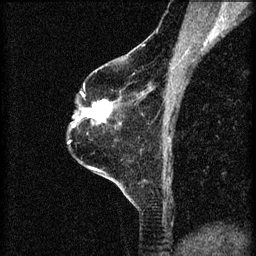
Breast MRI (dynamic contrast-enhanced), one sagittal slice; position 44 of 60 along the scan axis; 3 images stored at this slice position (order not interpretable as contrast timing); 1.5 T; TE 4.2 ms, TR 8.2 ms; 2 mm slice thickness; 256 × 256 image matrix, field of view 180 × 180 mm. Patient: female, 60 years.
Annotated regions visible in this slice (semi-automatically segmented with operator editing):
- analysis volume of interest (the breast-tissue region the enhancement analysis was run in; not a lesion): bounding box [x1, y1, x2, y2] px = [78, 94, 113, 125]
- tumour enhancement mask (voxels above the 70 % enhancement threshold inside the analysis volume of interest): [81, 94, 112, 123]